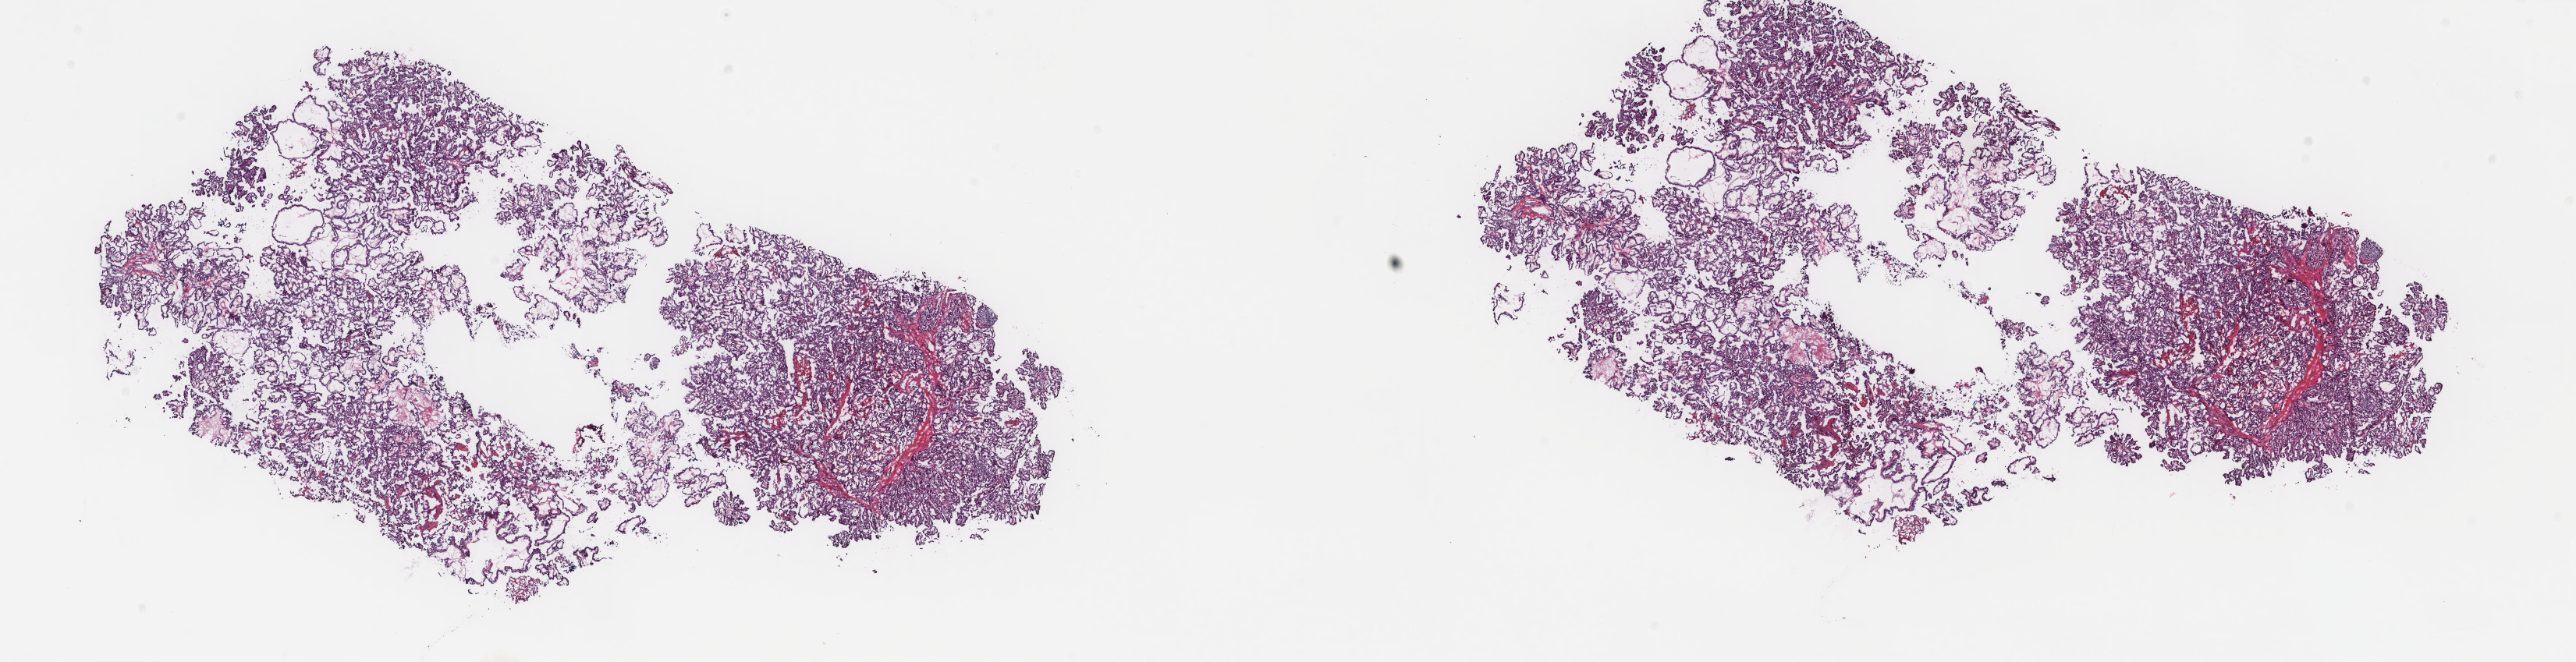
Whole-slide histology image, H&E-stained, shown as a low-resolution overview of the whole scanned area (about 26.2 x 6.7 mm), frozen section, primary tumour sample from the thyroid. Female, age 52 years at initial diagnosis. Pathologist review of this section (percent, as recorded): tumour cells 80%, tumour nuclei 80%, normal cells 0%, stromal cells 20%, necrosis 0%. Inflammatory infiltration, as recorded: lymphocyte infiltration 2%, monocyte infiltration 0%, neutrophil infiltration 0%.
* TNM: T1b N1a M0
* lymph nodes positive (case pathology): 3 of 5 examined
* AJCC pathologic stage: III (7th edition)
* pathologic diagnosis: Papillary adenocarcinoma, NOS